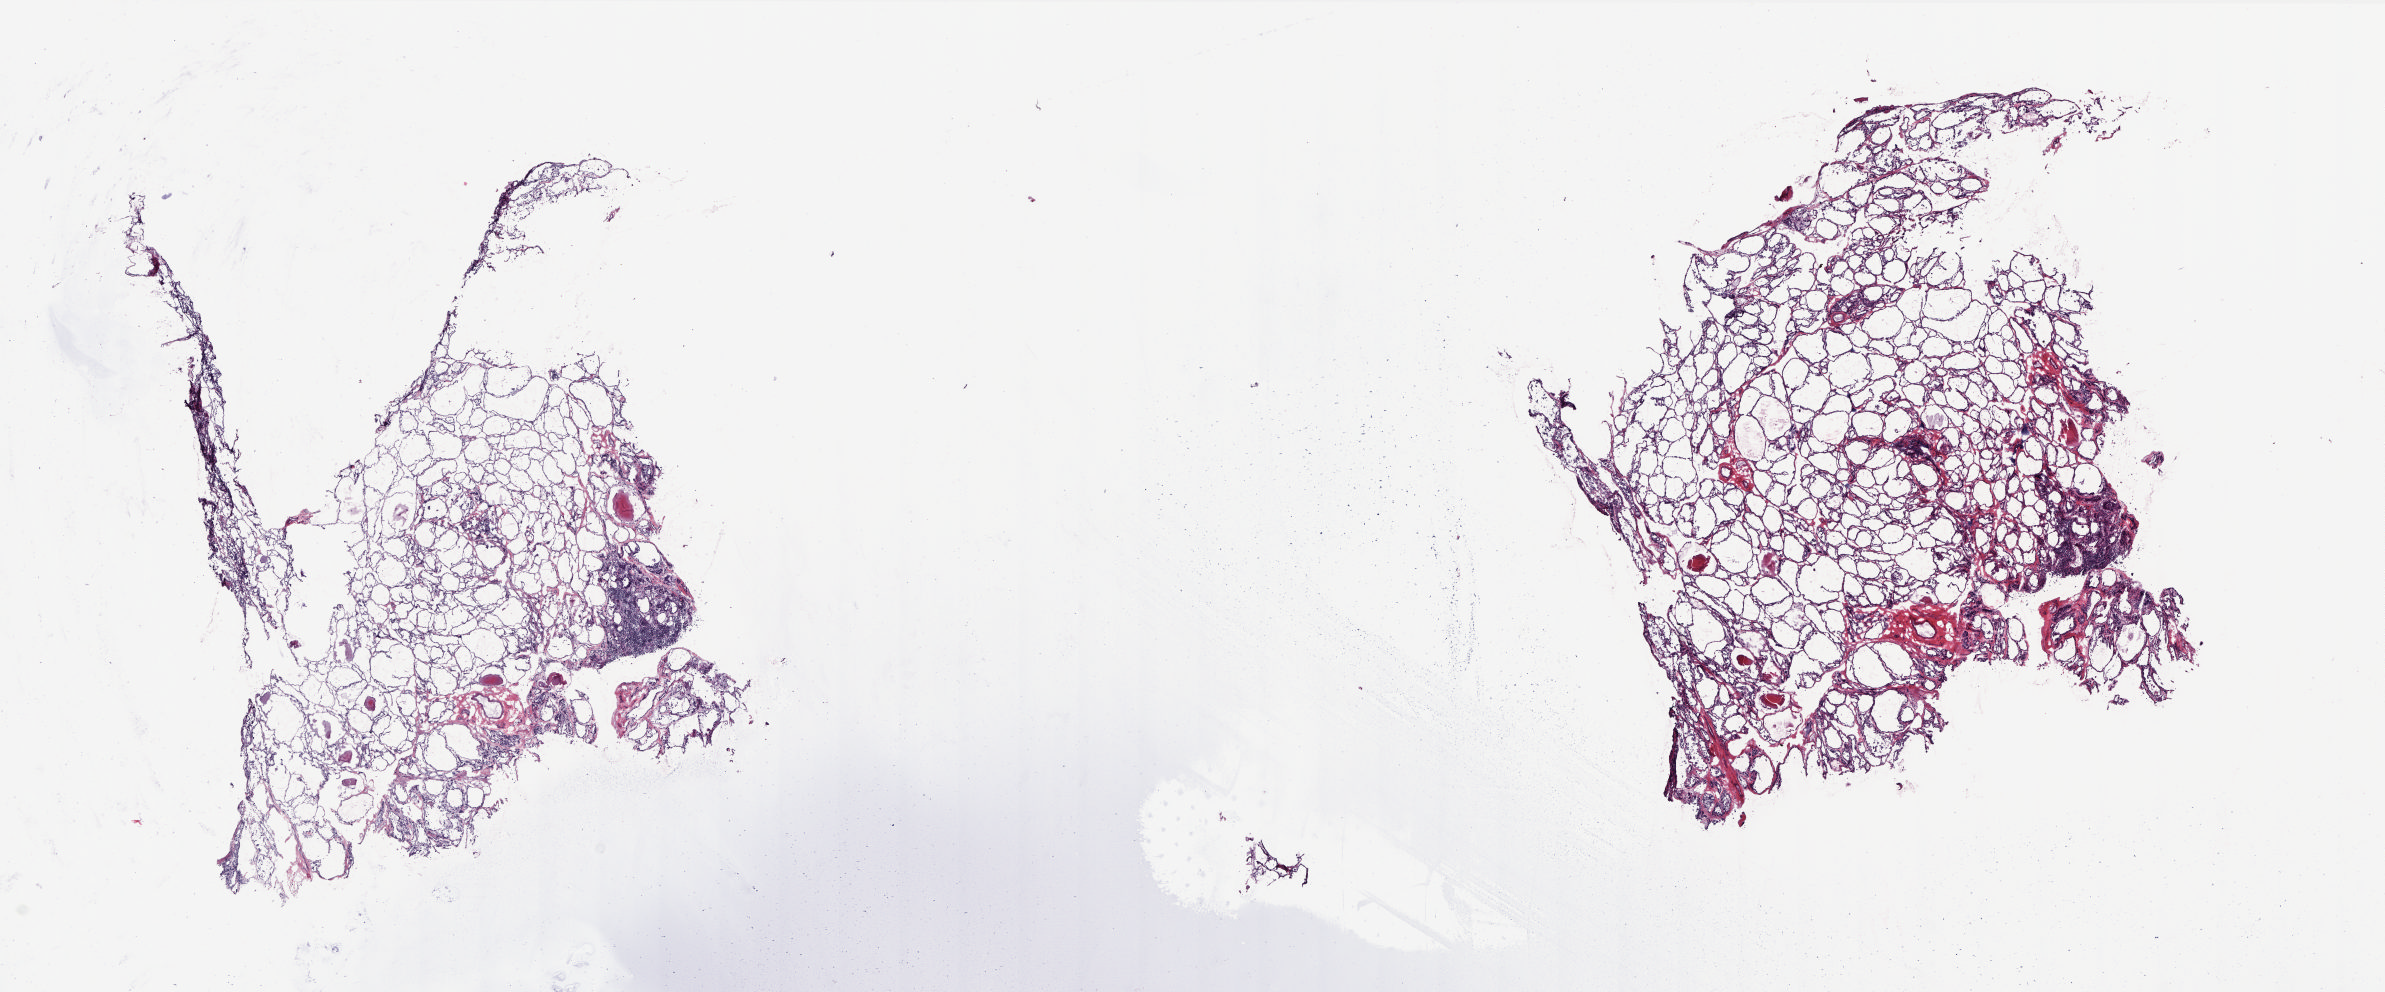
H&E-stained whole-slide image — a low-resolution overview of the entire scanned area, about 19.2 x 8.0 mm (from a 20x scan); frozen section; thyroid, solid tissue normal (non-tumour tissue) sample. Patient: female, age at initial diagnosis 38 years. Pathologist review of this section (percent, as recorded): tumour cells 0%, tumour nuclei 0%, normal cells 100%, stromal cells 0%, necrosis 0%. Infiltration values recorded for this section: lymphocyte infiltration 5%, monocyte infiltration 2%, neutrophil infiltration 0%.
• this section: solid tissue normal sample (biorepository sample class)
• patient diagnosis: Papillary adenocarcinoma, NOS (thyroid gland)